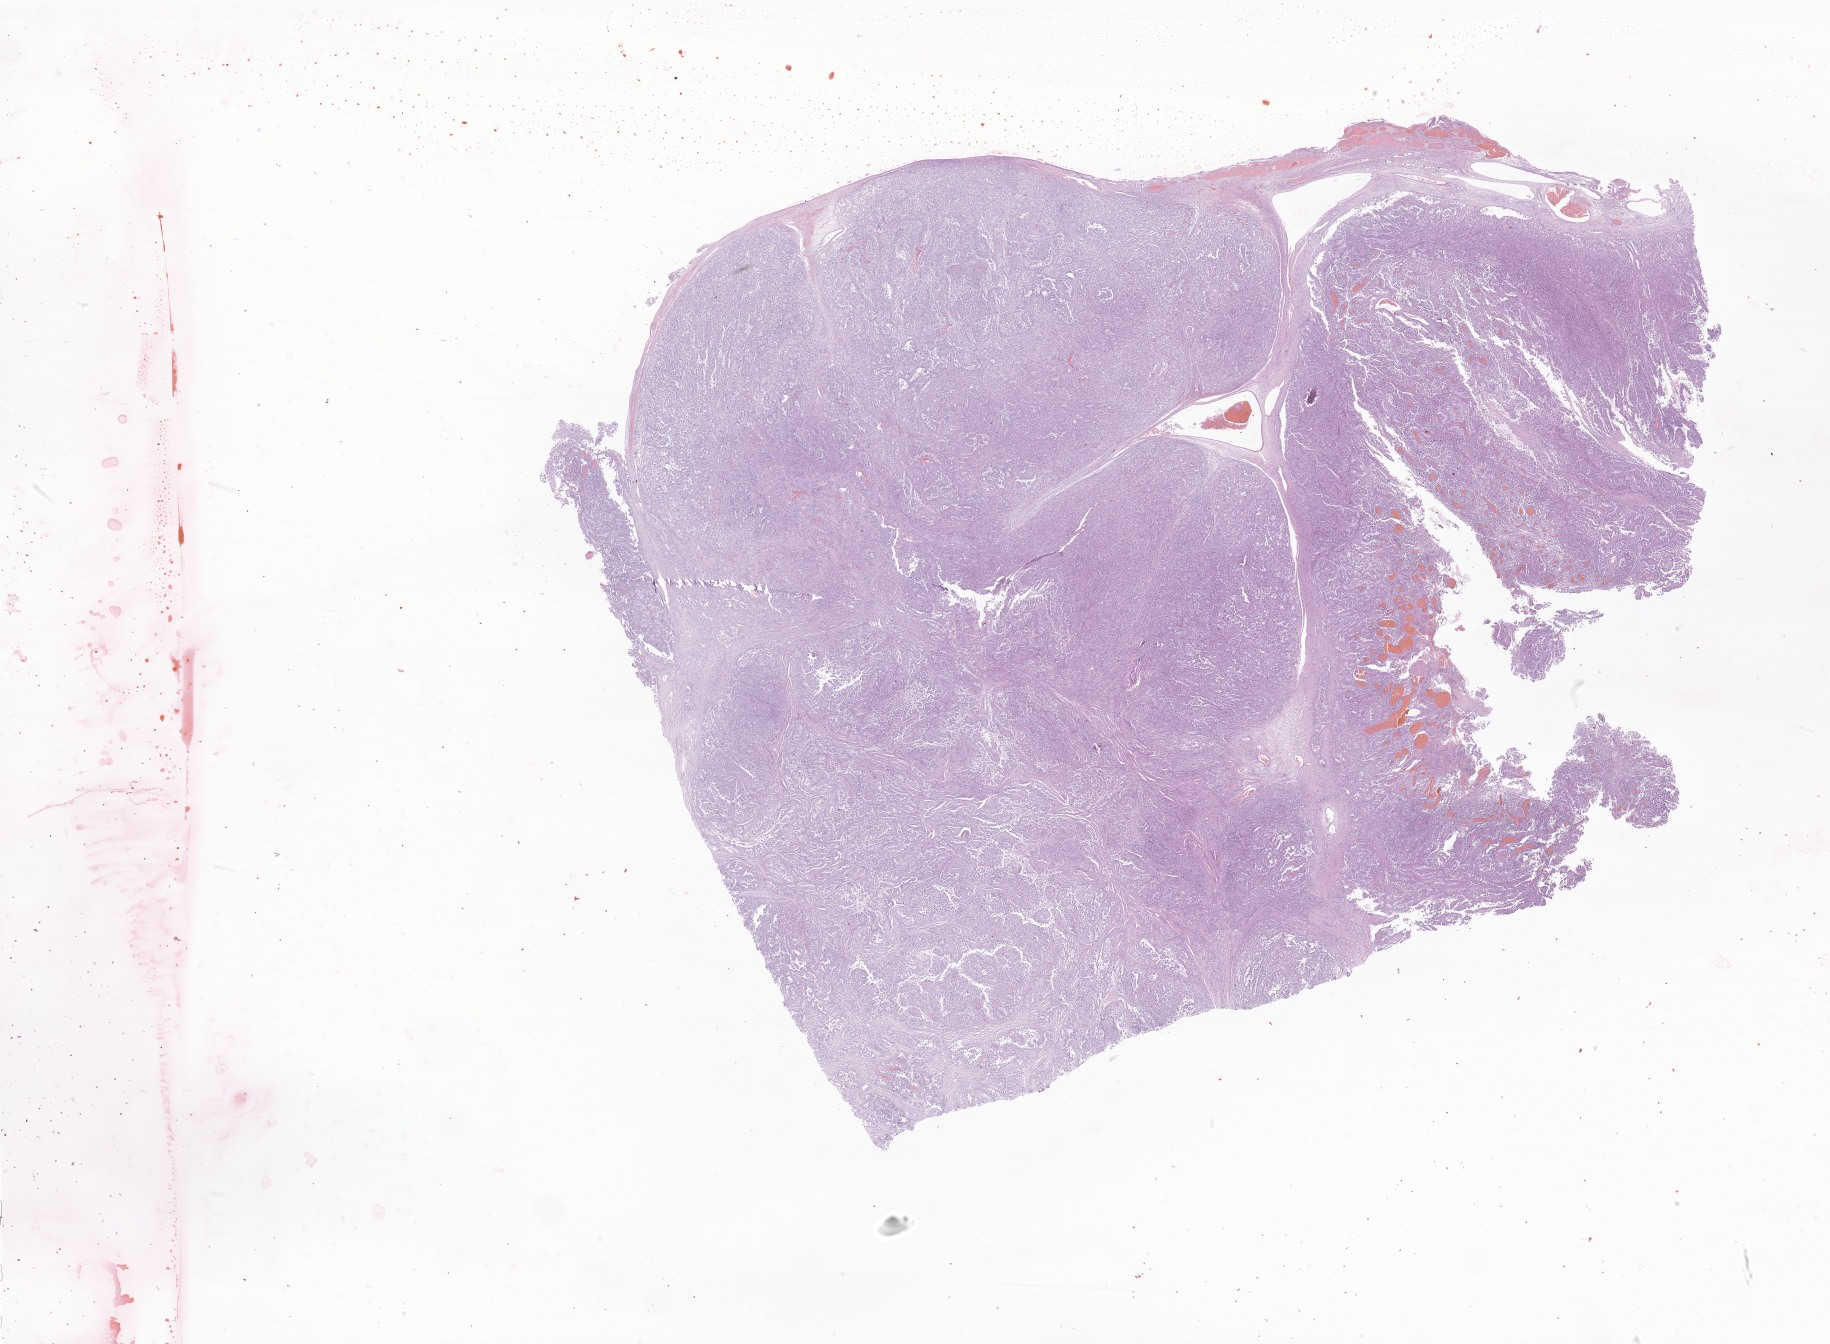
Digitized haematoxylin and eosin-stained section of tumor tissue from the parietal lobe — shown as a low-resolution overview of the whole scanned area (about 30.9 x 22.7 mm); formalin-fixed paraffin-embedded section. Patient male; age 174 days.
Recorded diagnosis: Choroid plexus carcinoma.